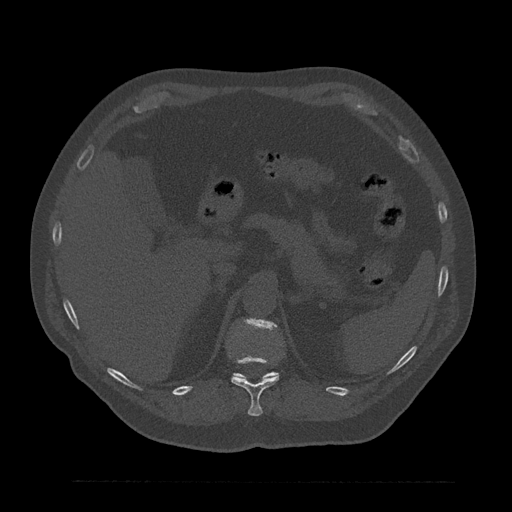
CT including the spine, one axial slice. Position 271 of 797 along the scan axis. Reconstruction kernel Br40s/3. 120 kVp. Bone window (W 1800 / L 400 HU). 0.5 mm slice thickness. 512 × 512 image matrix, field of view 430 × 430 mm. Patient: male, 61 years. From the clinical record (not read from this slice): primary cancer: prostate.
Structures marked on this image (semi-automatic segmentation, software-assisted and operator-edited):
- T11 vertebra: bounding box [x1, y1, x2, y2] px = [228, 351, 279, 416]
- T12 vertebra: [234, 319, 278, 379]